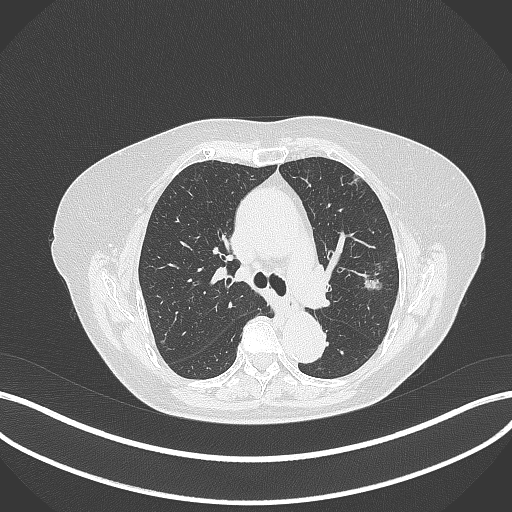
Chest CT, one axial slice; lung window (W 1500 / L -600 HU); 512 × 512 image matrix, field of view 400 × 400 mm. Patient: female, 75 years. Case-level facts recorded for this patient, not image findings: clinical TNM (as recorded): T1c N0 M0.
Outlined on this slice (rectangle marked by the reading radiologist):
- lung tumour (recorded histology: adenocarcinoma): bounding box <362,271,384,297> (left, top, right, bottom; pixels)